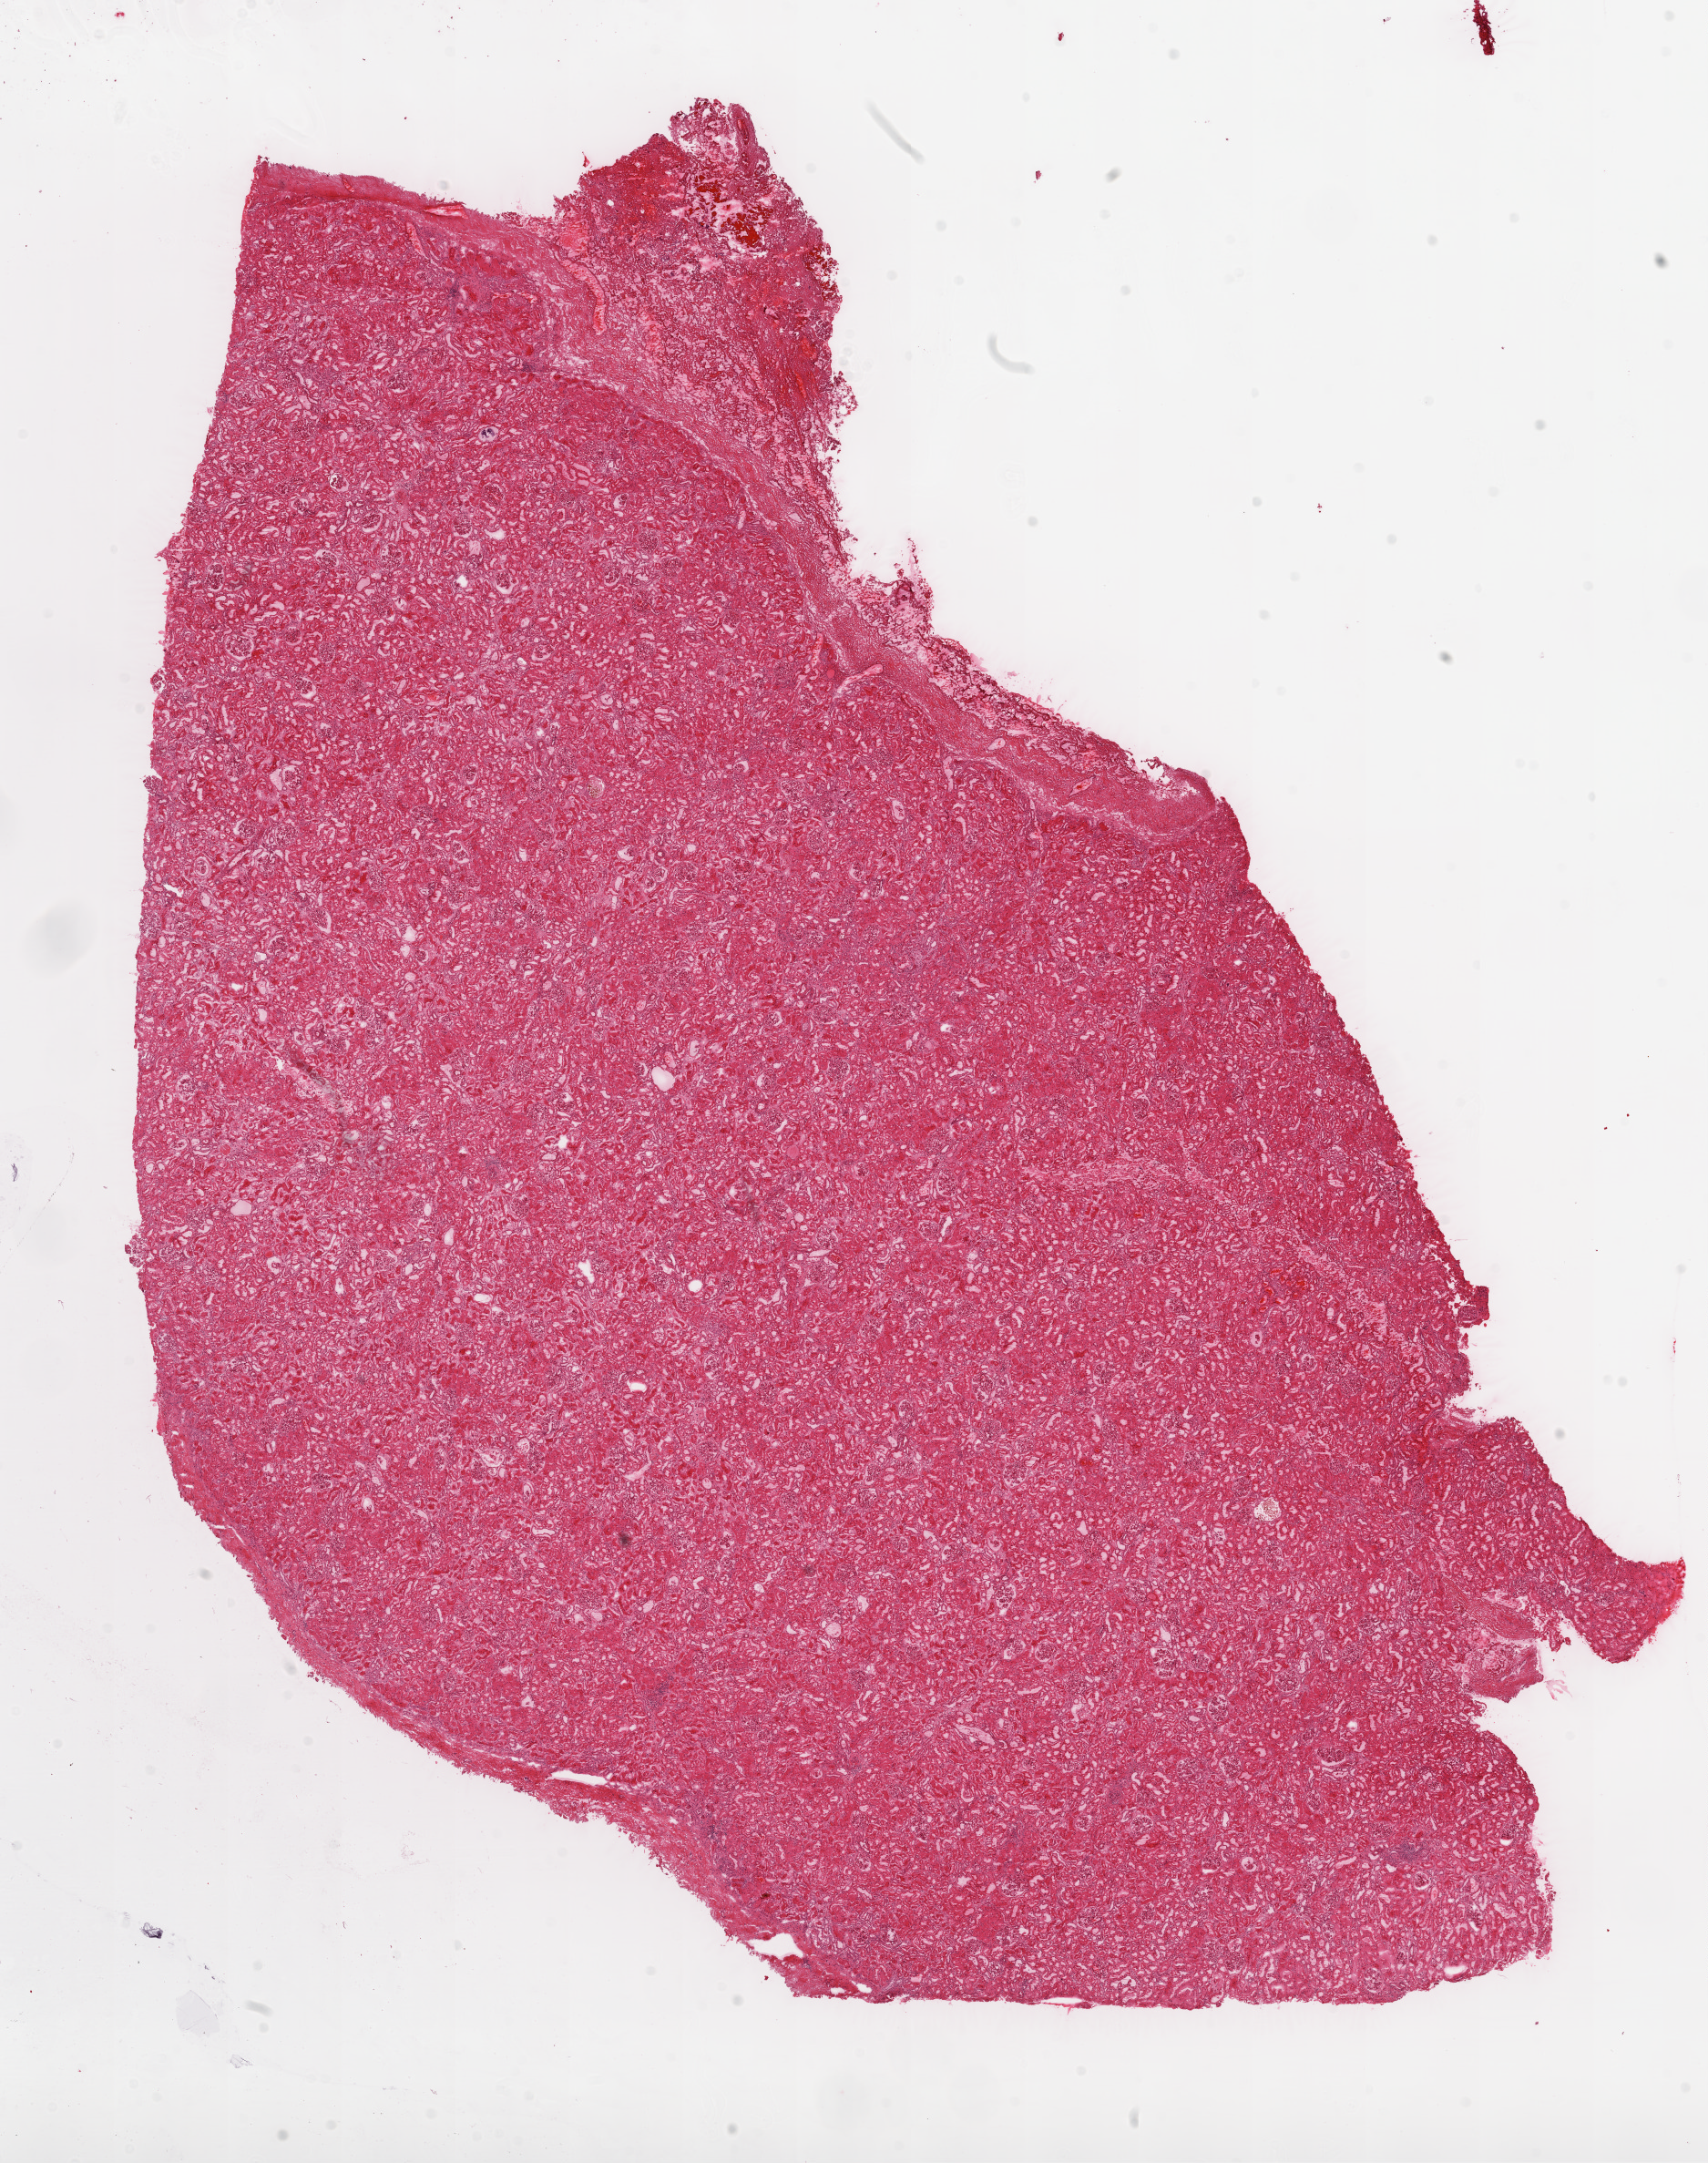
Whole-slide histology image, H&E-stained — low-resolution overview of the scanned area, about 15.0 x 19.0 mm (slide scanned at 20x), frozen section, solid tissue normal (non-tumour tissue) sample from the kidney. Female, age 72 years at initial diagnosis.
This section: solid tissue normal sample (biorepository sample class). Patient diagnosis: Clear cell adenocarcinoma, NOS.